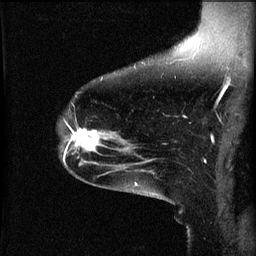
Breast MRI (dynamic contrast-enhanced), one sagittal slice. Slice 41 of 60 in the series (ordered by position). 3 images stored at this slice position (order not interpretable as contrast timing). 1.5 T. TE 4.2 ms, TR 8.2 ms. 2 mm slice thickness. 256 × 256 image matrix, field of view 200 × 200 mm. Female patient, age 49 years.
Outlined on this slice (semi-automatically segmented with operator editing):
- analysis volume of interest (the breast-tissue region the enhancement analysis was run in; not a lesion): bounding box <66,124,113,157> (left, top, right, bottom; pixels)
- tumour enhancement mask (voxels above the 70 % enhancement threshold inside the analysis volume of interest): <66,130,107,151>